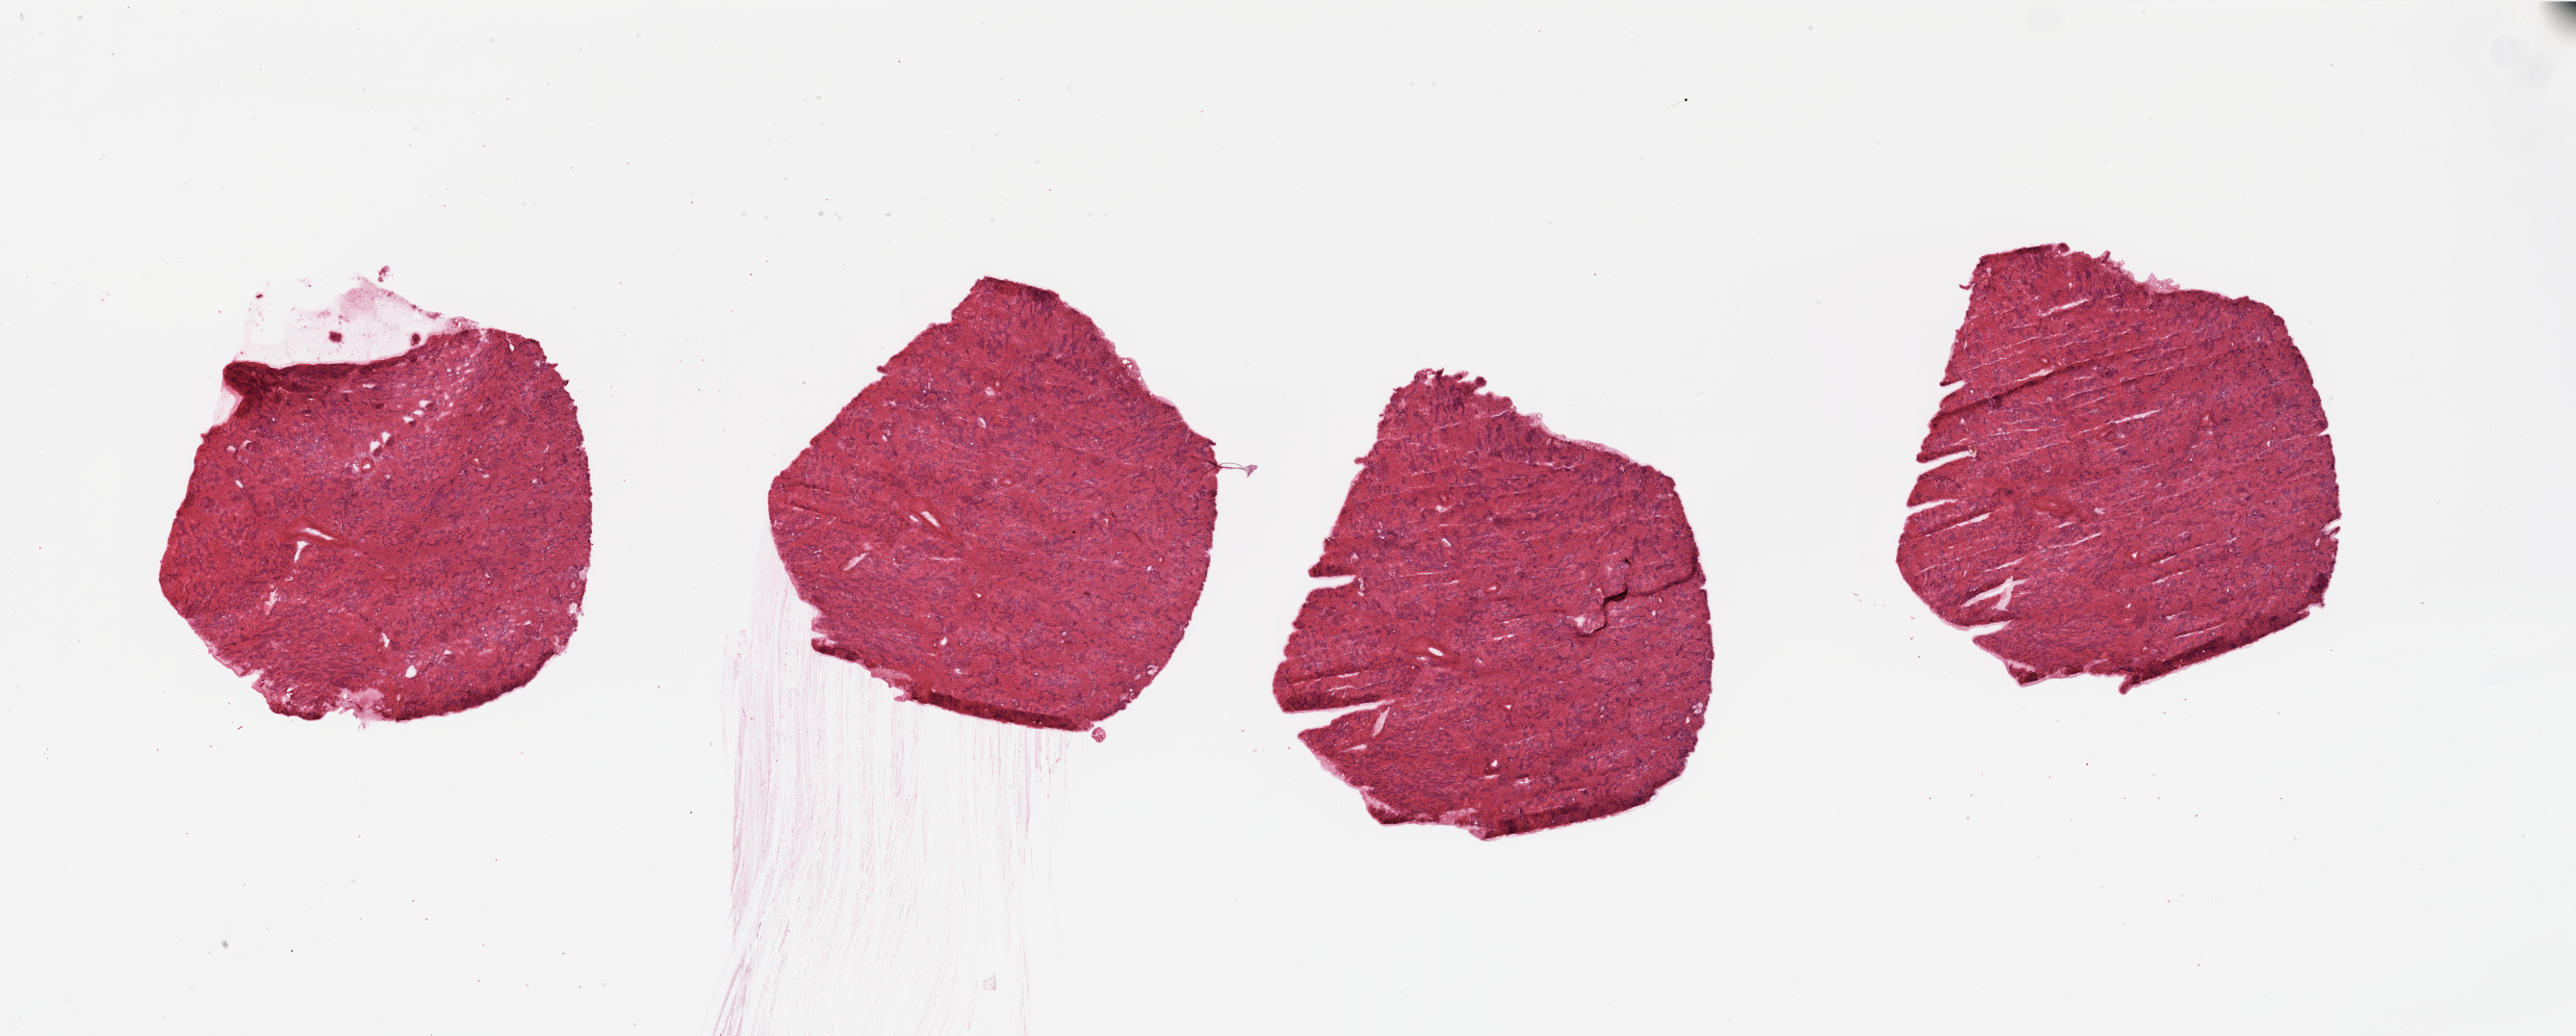
H&E-stained whole-slide image — whole scanned area (about 42.3 x 17.0 mm) shown as a low-resolution overview. Normal (non-tumour) tissue sample, kidney. Patient: male, age 54 years.
This section: normal (non-tumour) tissue from the same patient. Patient diagnosis: Renal cell carcinoma, NOS.